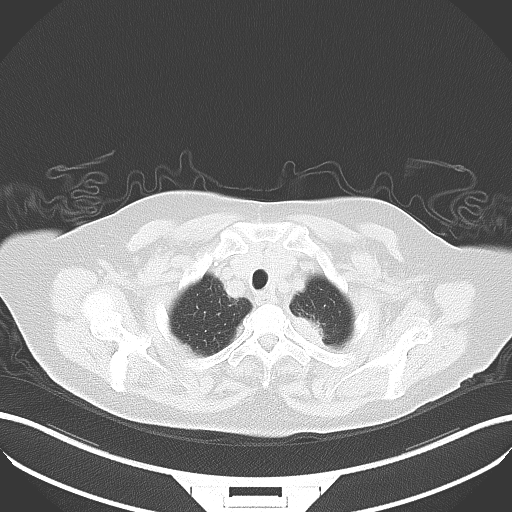
Chest CT, one axial slice; position 37 of 42 along the scan axis; lung window (W 1500 / L -600 HU); 6 mm slice thickness; 512 × 512 image matrix, field of view 400 × 400 mm. Patient: female, 81 years. Case-level facts recorded for this patient, not image findings: clinical TNM (as recorded): T2a N0 M0.
Outlined on this slice (rectangle marked by the reading radiologist):
- lung tumour (recorded histology: adenocarcinoma): bounding box (x1, y1, x2, y2) in pixels: (287, 312, 337, 354)